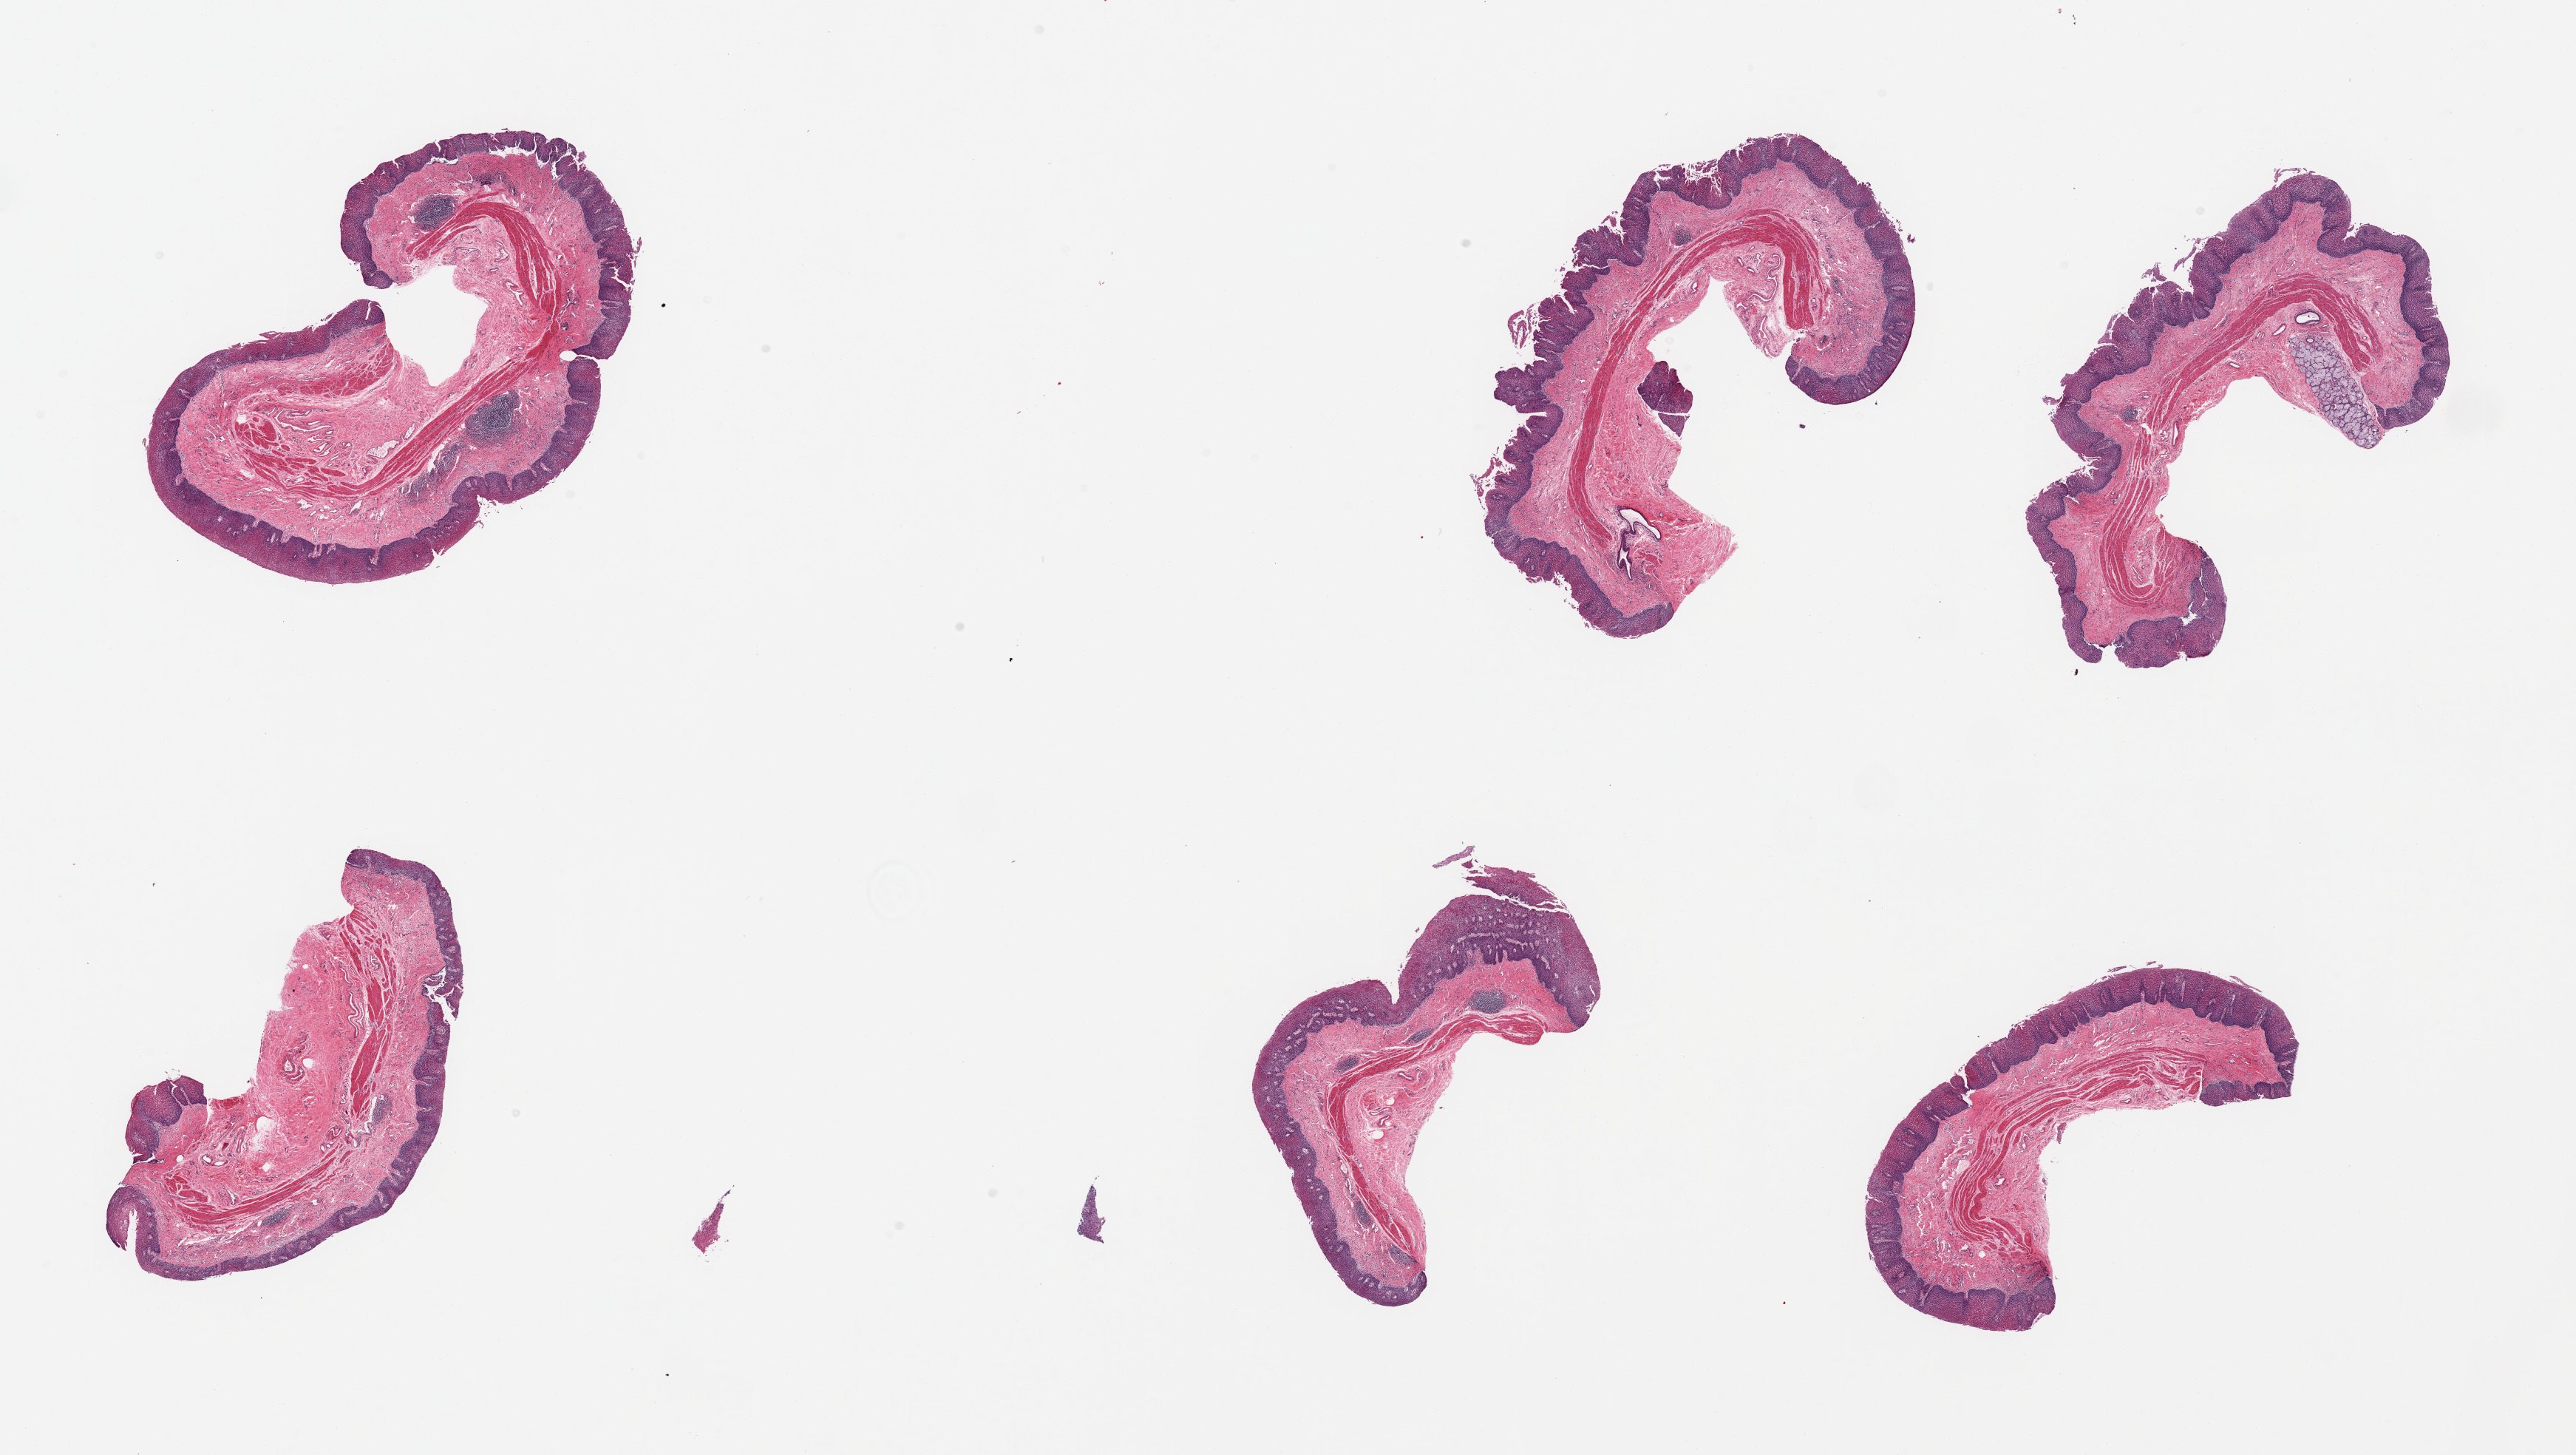
Hematoxylin and eosin (H&E) whole-slide image — a low-resolution overview of the entire scanned area, about 27.6 x 15.6 mm (acquisition: 20x scan); PAXgene-fixed, paraffin-embedded tissue; sampled site (target tissue): esophageal mucous membrane; tissue donor sample. Donor: male.
Reviewer comment on this tissue sample: 6 pieces; well dissected; mild chronic inflammation with squamous hyperplasia; 1 submucosal gland.